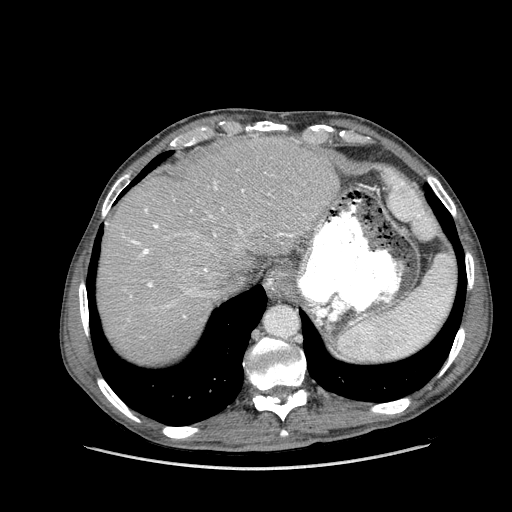
Contrast-enhanced abdominal CT (liver protocol), one axial slice; position 121 of 162 along the scan axis; 100 kVp; soft-tissue window (W 400 / L 40 HU); 2.5 mm slice thickness; 512 × 512 image matrix, field of view 400 × 400 mm. Case-level facts recorded for this patient, not image findings: diagnosis: hepatocellular carcinoma (patient treated with transarterial chemoembolisation; whether this scan precedes or follows treatment is not stated here); TNM stage (as recorded): Stage-IIIA; Child-Pugh class: A; tumour nodularity: multinodular; tumour size: 9.9 cm.
Outlined on this slice (semi-automatic segmentation, software-assisted and operator-edited):
- abdominal aorta: bounding box <266,307,297,337> (left, top, right, bottom; pixels)
- liver parenchyma outside the tumour (the mass and vessels are separate outlines, so this box may not span the whole liver): <97,136,338,362>
- liver vessels: <131,182,293,318>